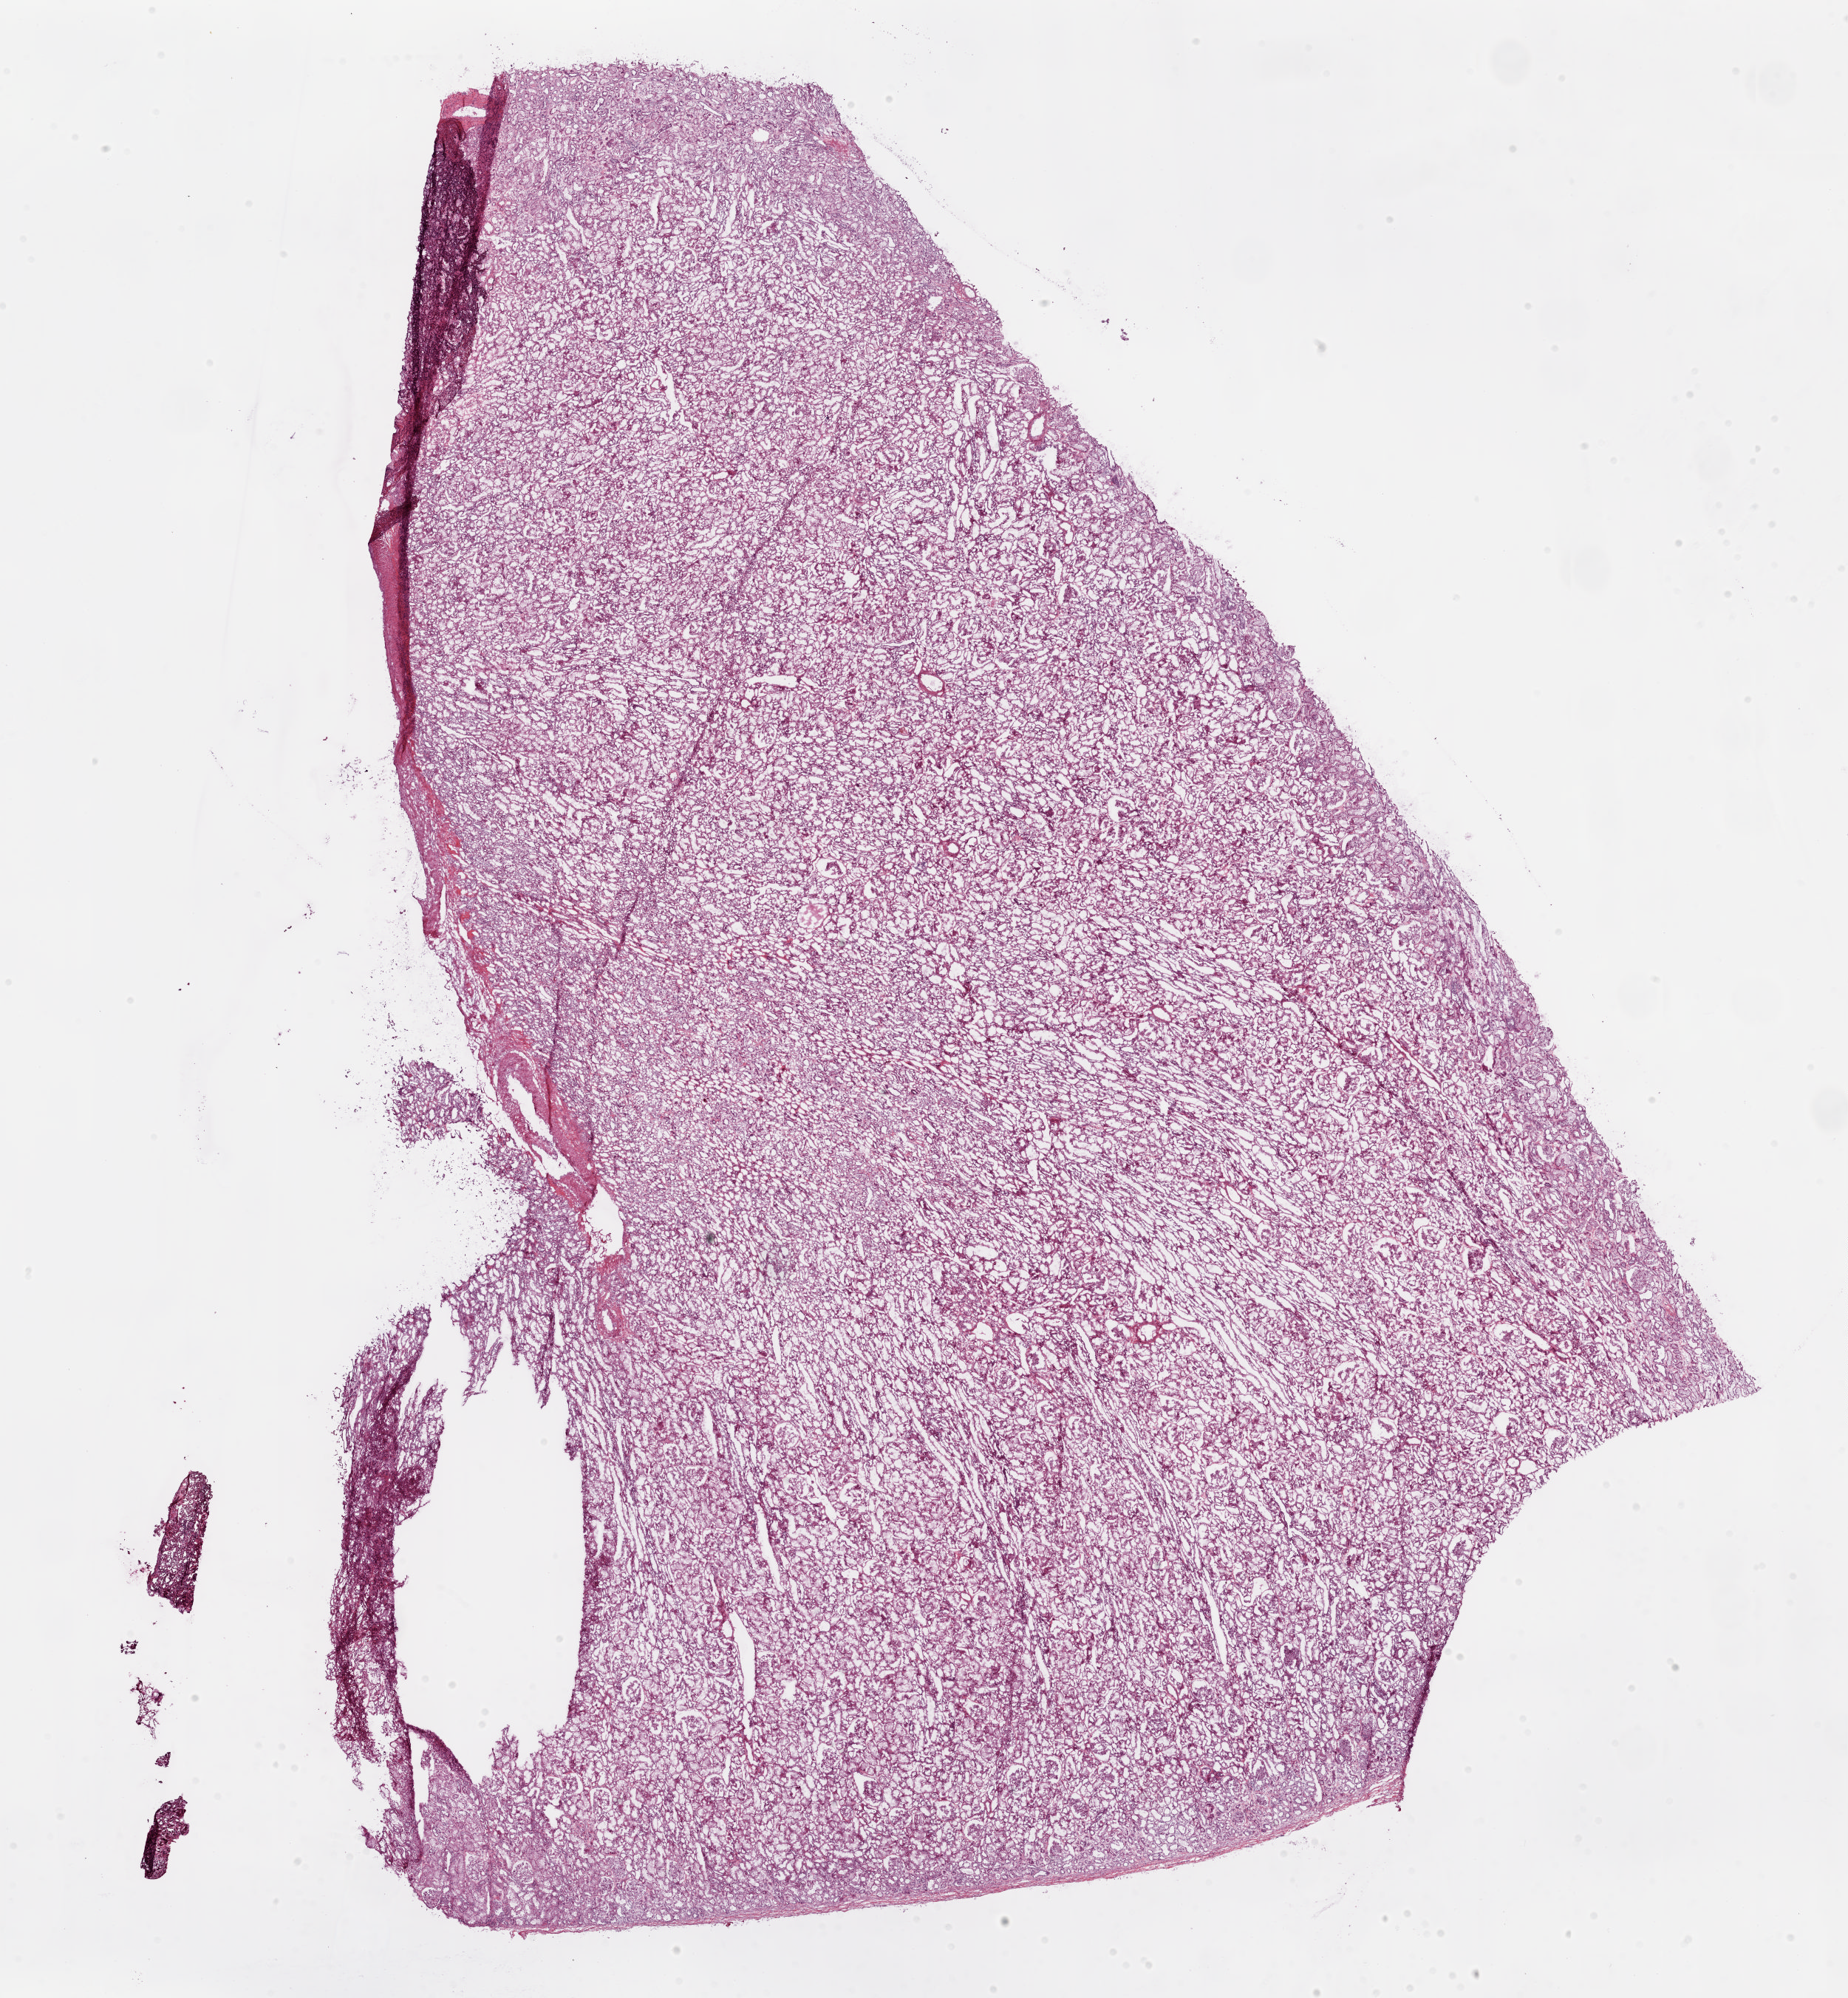
Whole-slide histology image, H&E, a low-resolution overview of the entire scanned area, about 19.8 x 21.4 mm (slide scanned at 20x); frozen section from the bottom of the tissue portion; kidney, solid tissue normal (non-tumour tissue) sample. Patient: male, age at initial diagnosis 51 years.
• this section: solid tissue normal (non-tumour) sample from the same patient
• patient diagnosis: Clear cell adenocarcinoma, NOS